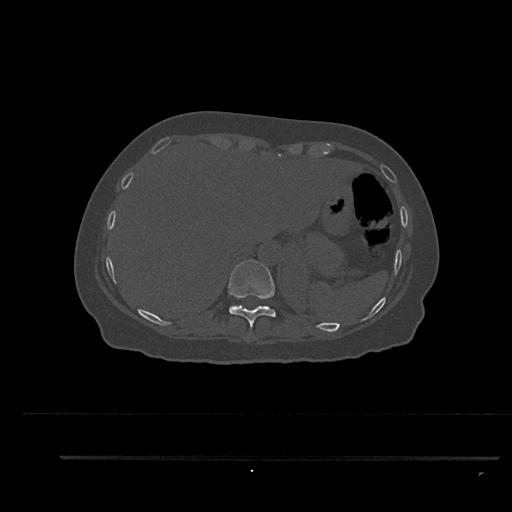
CT including the spine, one axial slice. Slice 359 of 797 in the series (ordered by position). Bone window (W 1800 / L 400 HU). 0.5 mm slice thickness. 512 × 512 image matrix. Female patient, age 44 years. From the clinical record (not read from this slice): primary cancer: renal; vertebrae with lytic lesions (as recorded): L1.
Annotated regions visible in this slice (semi-automatically segmented with operator editing):
- T10 vertebra: bounding box <228,260,276,331> (left, top, right, bottom; pixels)